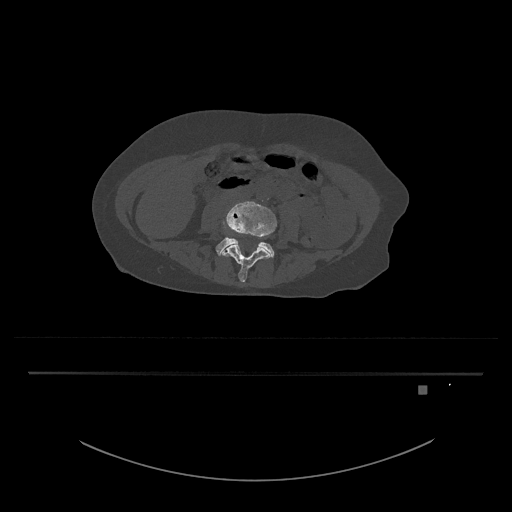
CT including the spine, one axial slice; slice 341 of 797 in the series (ordered by position); bone window (W 1800 / L 400 HU); 0.5 mm slice thickness; 512 × 512 image matrix, field of view 500 × 500 mm. Patient: female, 57 years. Case-level facts recorded for this patient, not image findings: primary cancer: cervical.
Outlined on this slice (semi-automatically segmented with operator editing):
- L4 vertebra: bounding box <220,201,277,282> (left, top, right, bottom; pixels)